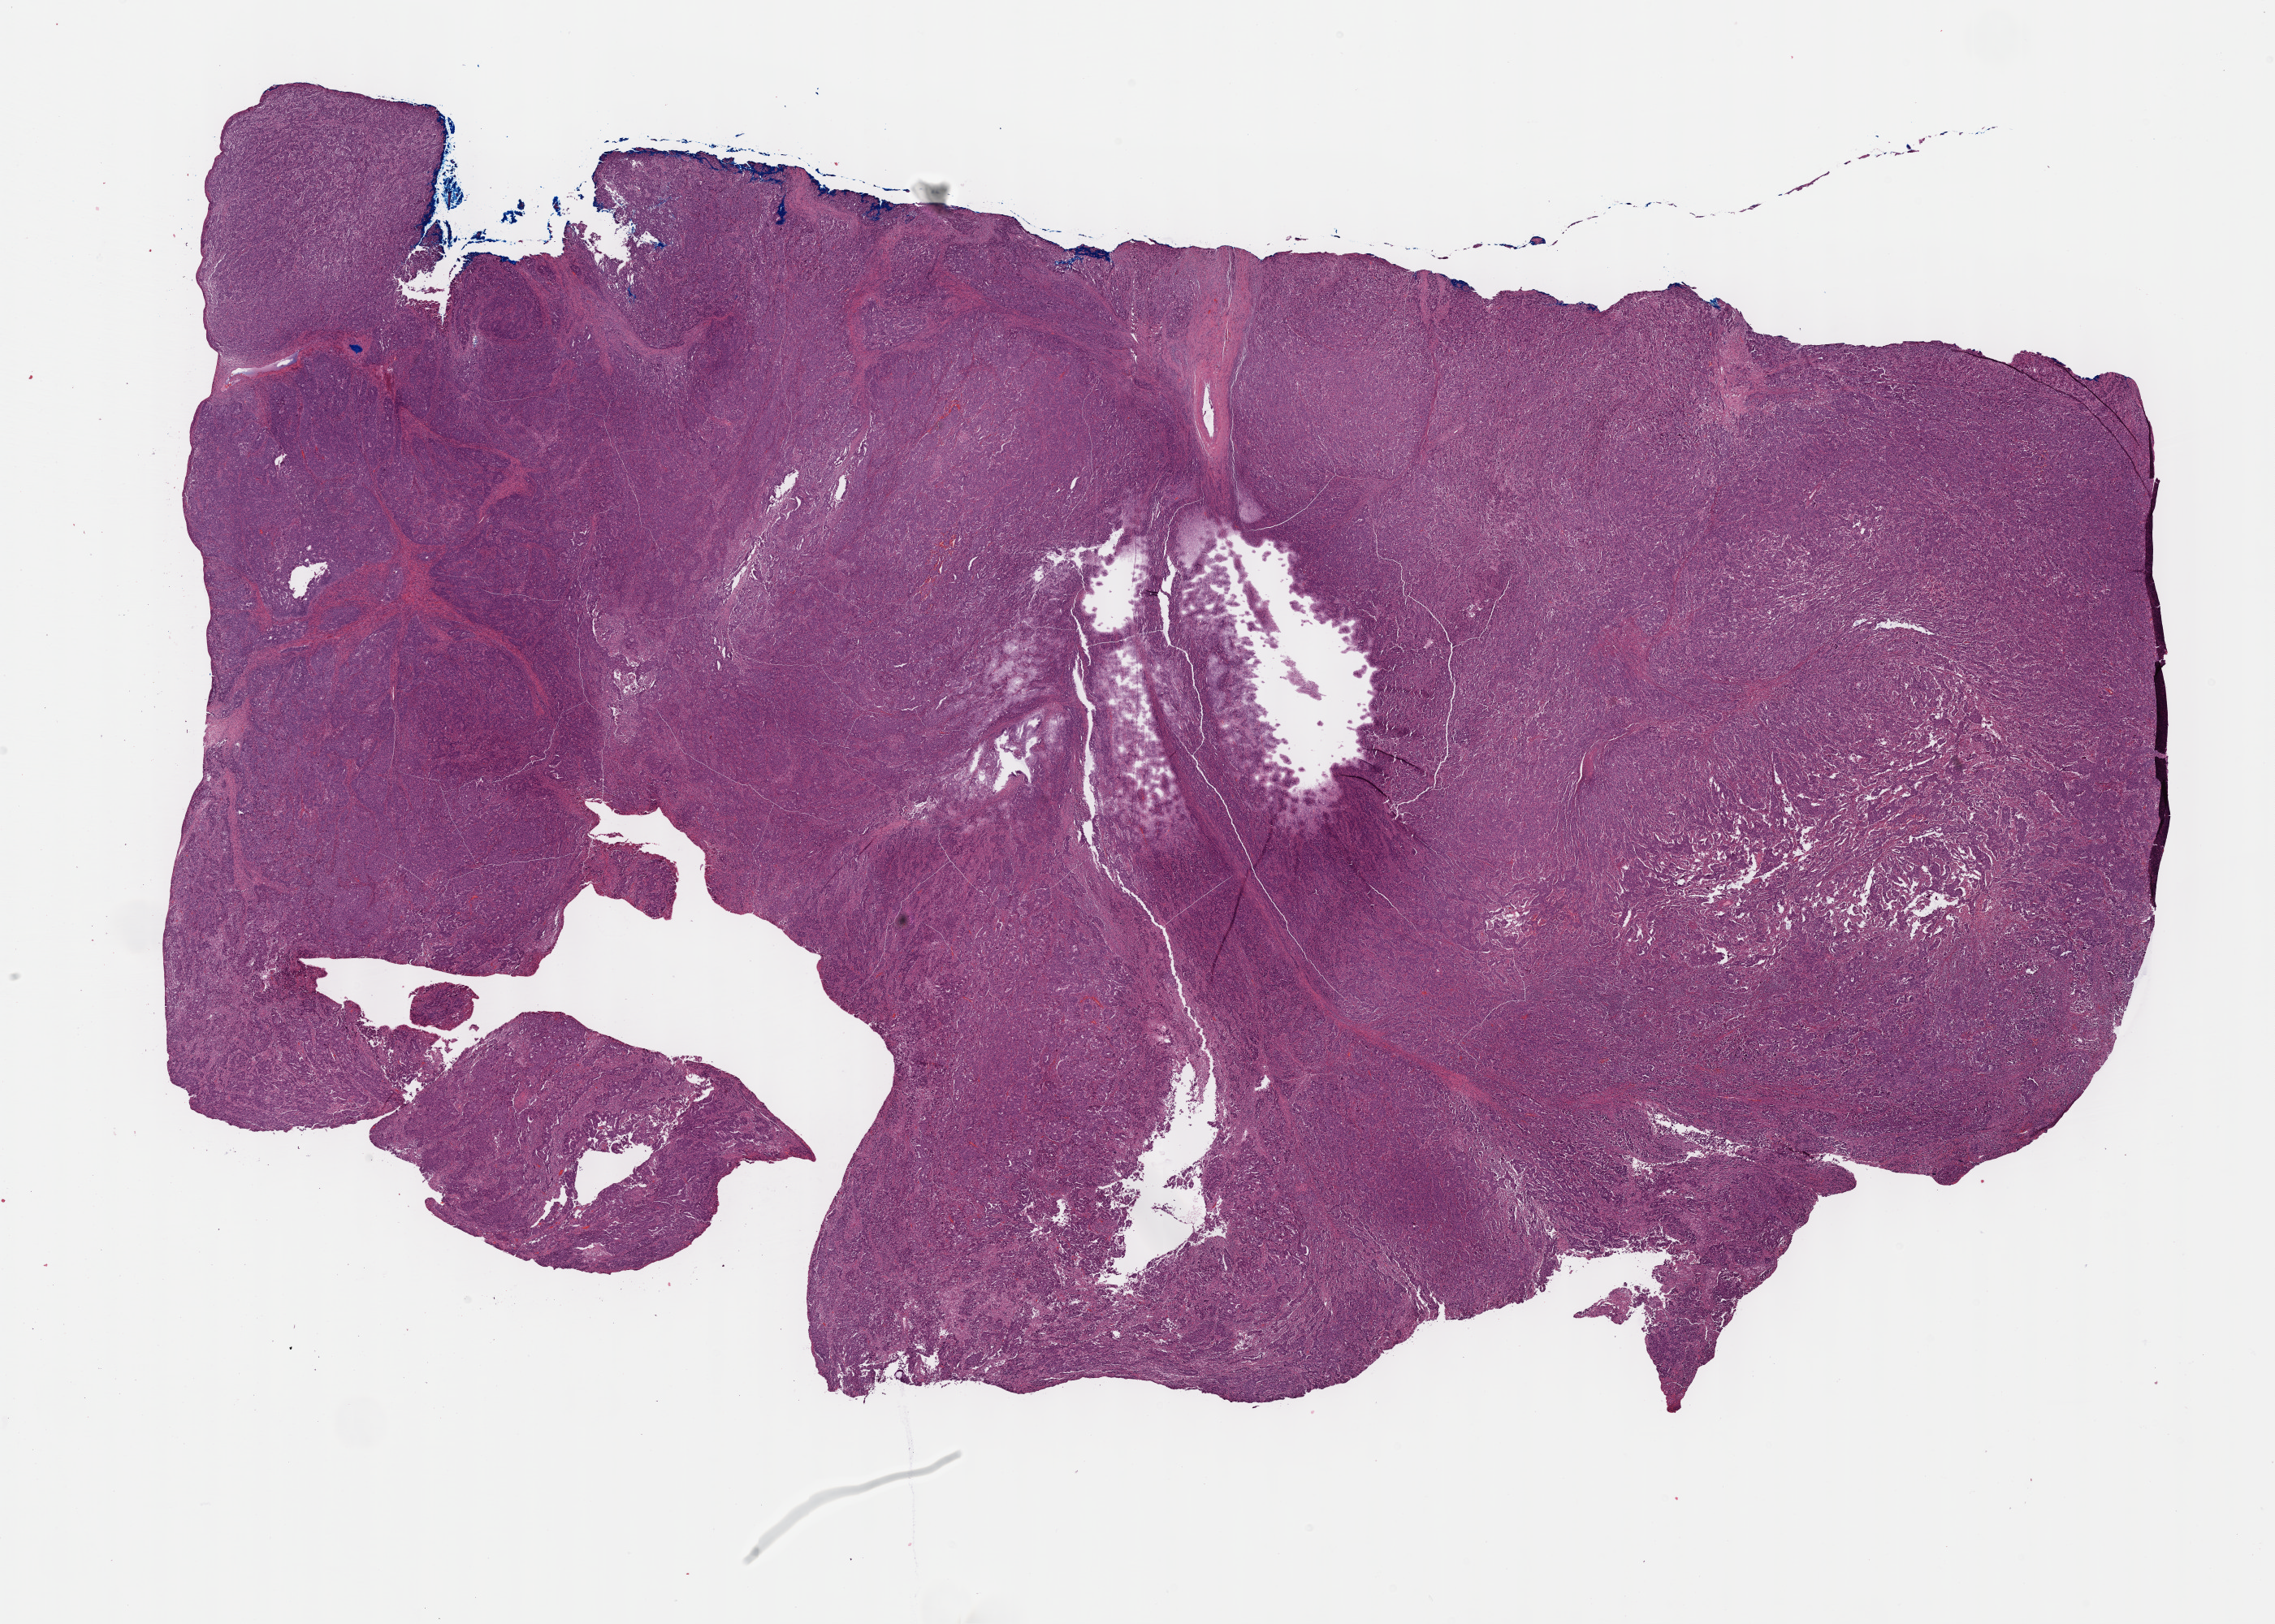
Digitized Hematoxylin and eosin (H&E) stained tissue section (whole slide) — shown as a low-resolution overview of the whole scanned area (about 22.7 x 16.2 mm, from a 40x scan); formalin-fixed paraffin-embedded (FFPE) diagnostic section; sample: primary tumour, uterus. Female patient; age at initial diagnosis 73 years. Histologic grade: G3 (poorly differentiated).
- FIGO stage: IB
- pathologic diagnosis: Endometrioid adenocarcinoma, NOS (endometrium)